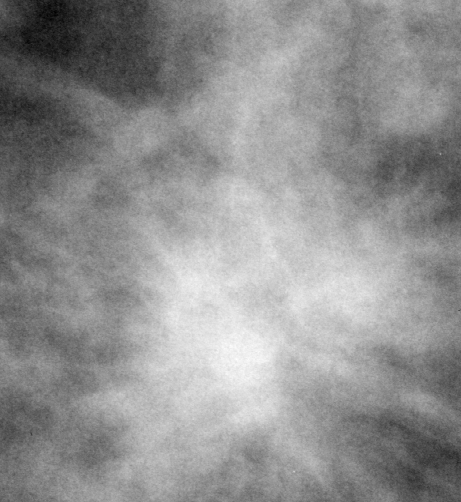
Region of interest cut from a scanned film mammogram (one marked finding); left breast; MLO view.
Marked abnormality: mass, shape architectural distortion, margins spiculated; BI-RADS assessment category 5; pathology (as recorded): malignant.